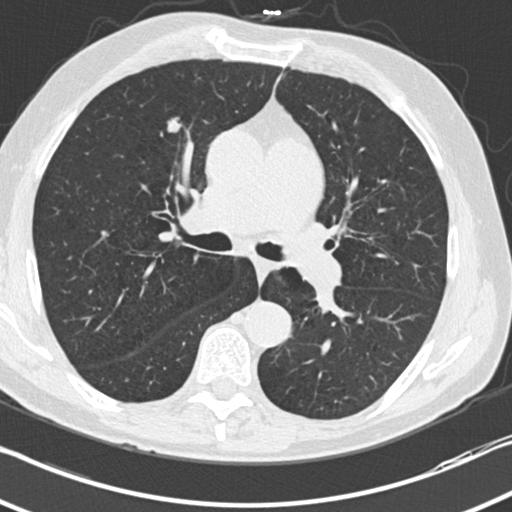
Low-dose screening chest CT, axial slice; third annual screen; lung window (W 1500 / L -600 HU); 2 mm slice thickness; standard (soft-tissue) reconstruction kernel (B30f); 120 kVp; 512 × 512 image matrix. Male, age 70 years at enrolment.
Lesion marked by an expert reader, bounding box (x1, y1, x2, y2) in pixels: (156, 108, 197, 143). The exam's reader record, not a measurement of the box and not confirmed to be the same lesion: non-calcified nodule or mass ≥4 mm, right middle lobe, 9 × 8 mm, smooth margins, soft tissue attenuation, pre-existing on the prior screen: no. Official screen result: positive, other. Lung cancer was diagnosed 53 days after this screen: squamous cell carcinoma, NOS, right upper lobe, moderately differentiated (G2), stage IA (AJCC 6th edition), 10 mm at pathology.